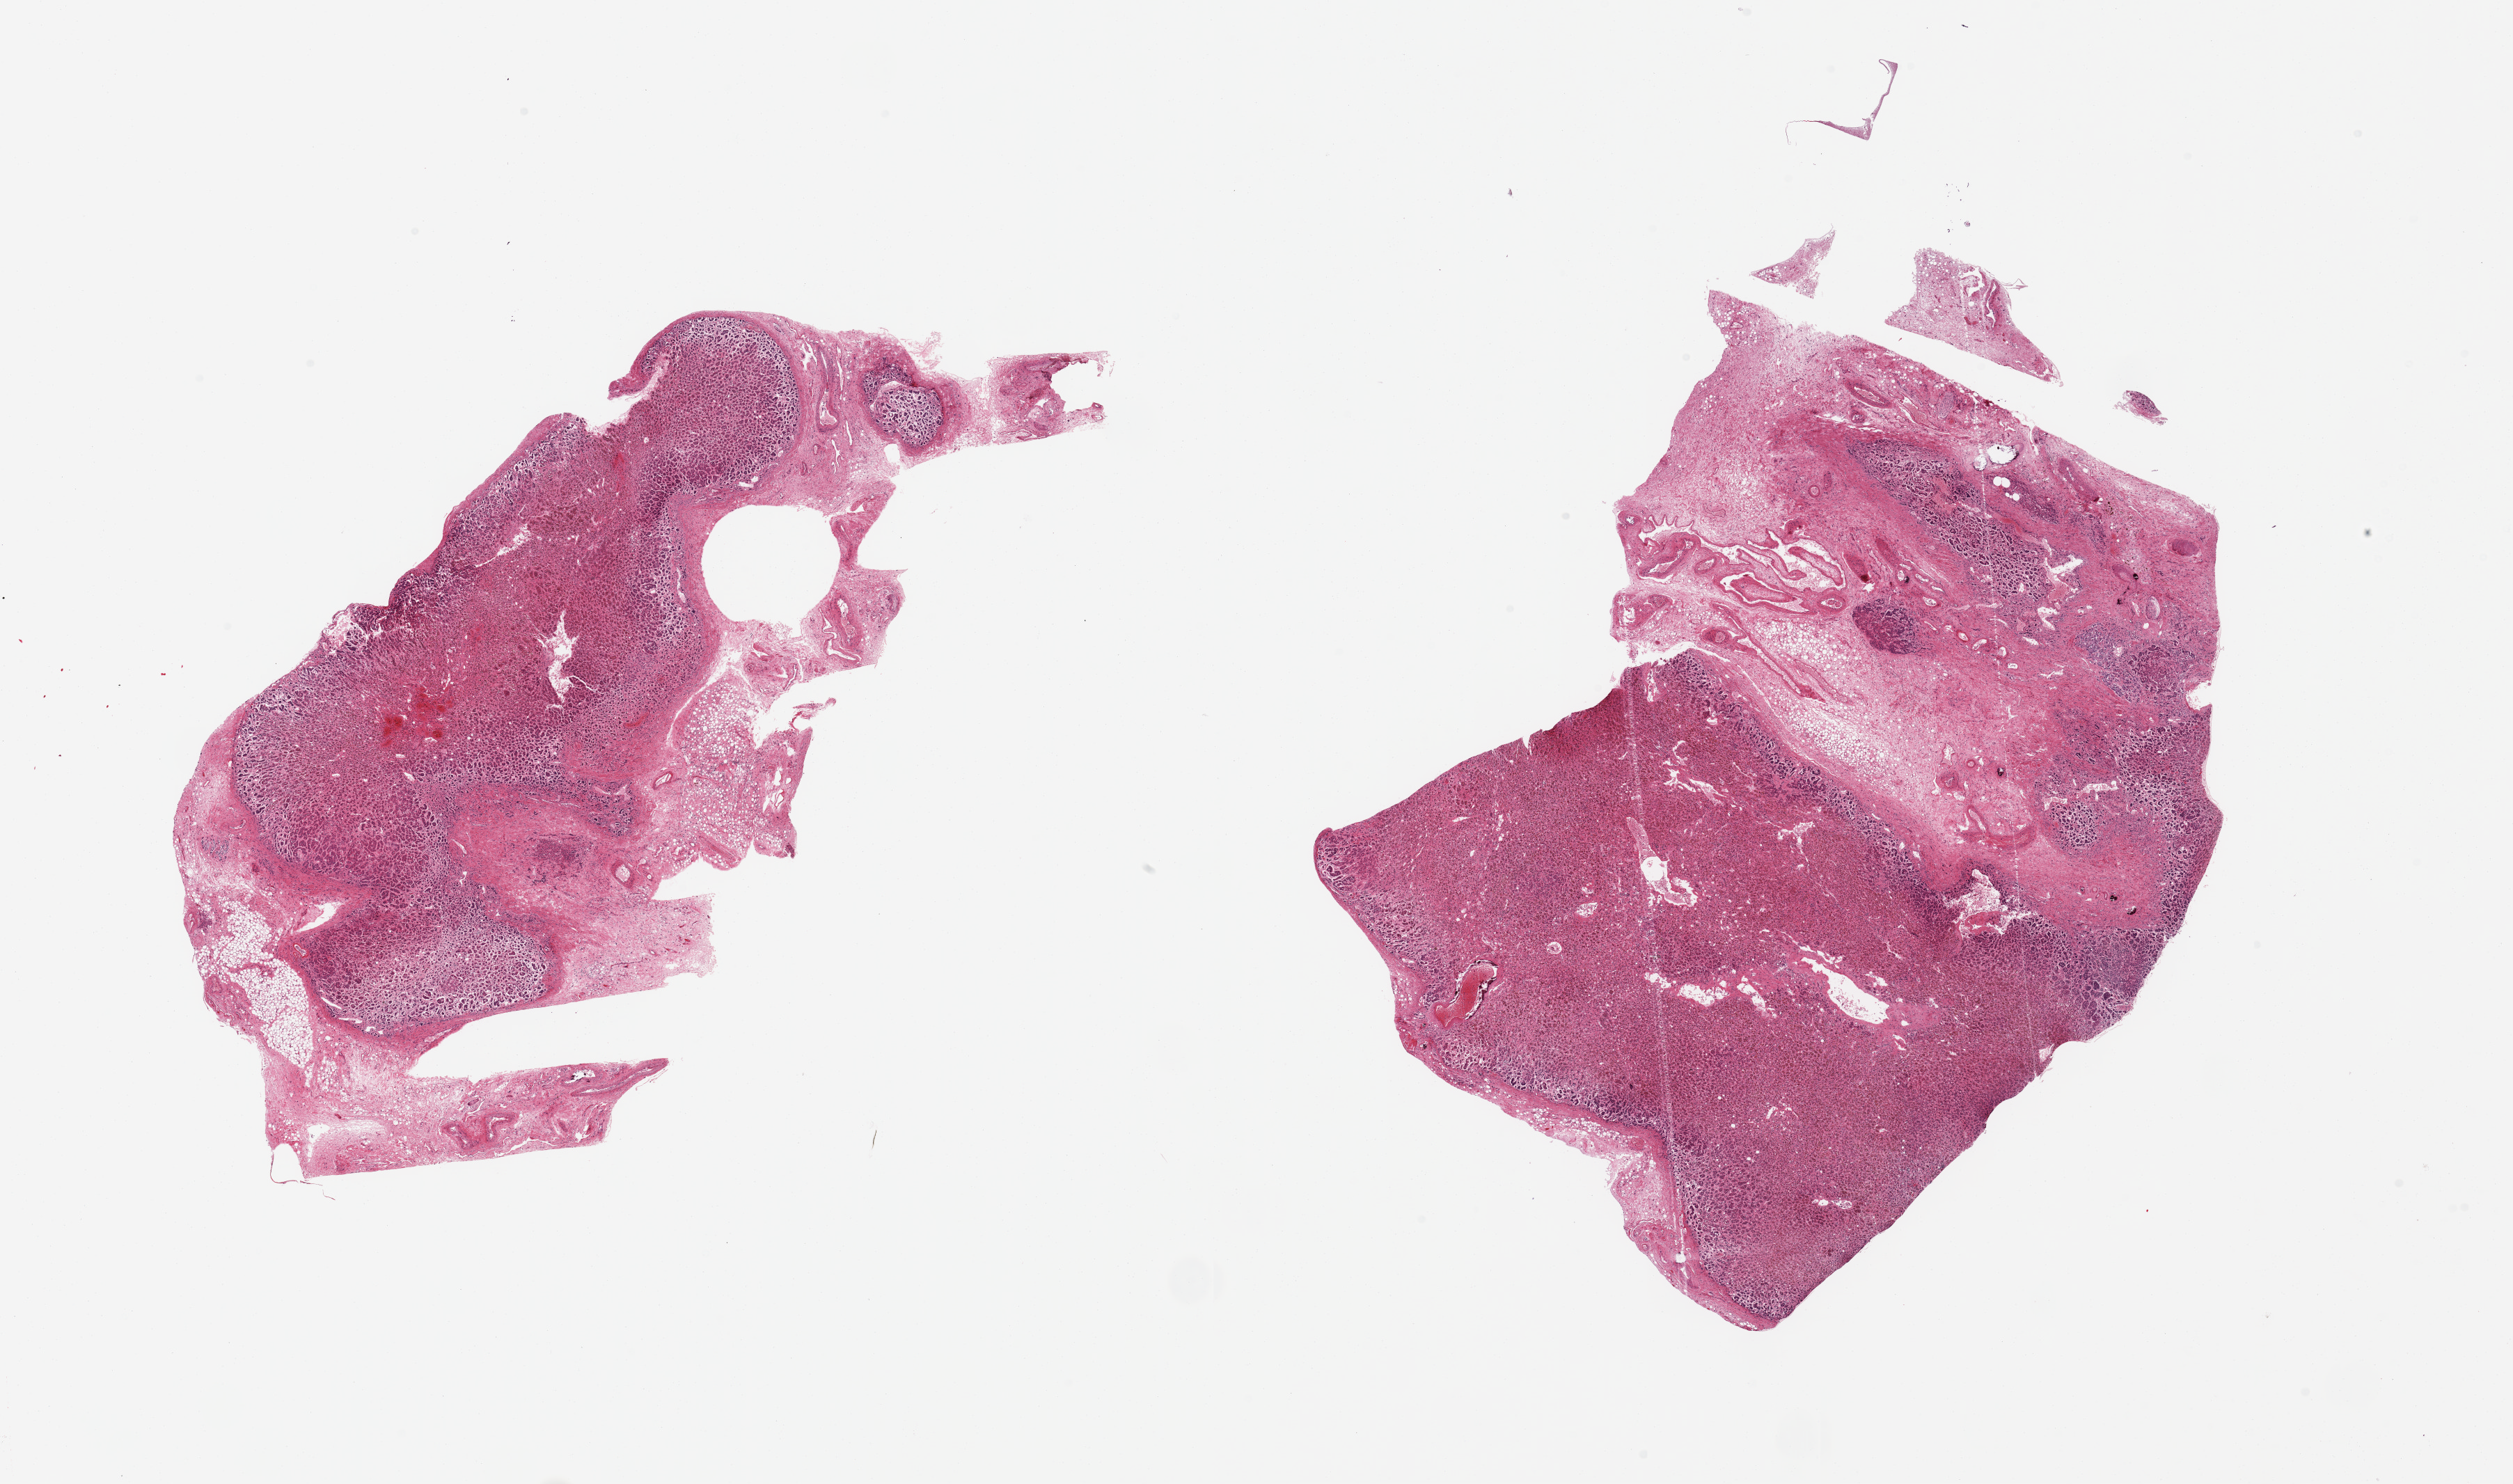
Hematoxylin and eosin (H&E) whole-slide image, shown as a low-resolution overview of the whole scanned area (about 28.5 x 16.9 mm). PAXgene-fixed, paraffin-embedded tissue. Sampled site (target tissue): adrenal gland. Tissue donor sample. Female donor.
- reviewer comment on this tissue sample: 2 pieces, cortex, adferent fat is ~30% of tissue